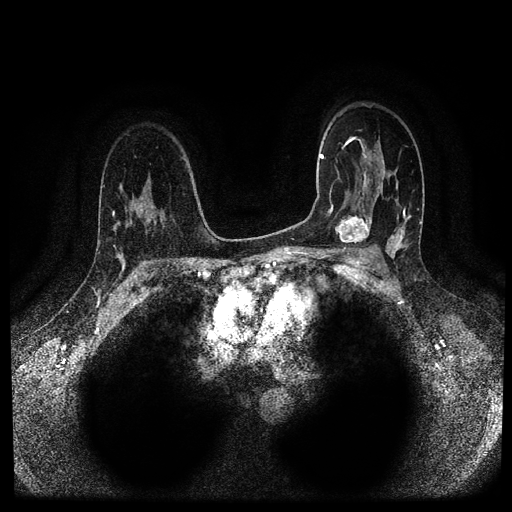
Breast MRI (dynamic contrast-enhanced, multi-phase), one axial slice; slice 69 of 116 in the series (ordered by position); dynamic contrast-enhanced series, time point 2 of 5 at this slice position (early post-contrast); 1.5 T; TE 2.6 ms, TR 5.3 ms; 512 × 512 image matrix. Patient: female, 44 years.
Structures marked on this image (semi-automatic segmentation, software-assisted and operator-edited):
- breast lesion (labelled 'tumour' in the annotation; benign lesions carry a separate 'benign' label): bounding box [x1, y1, x2, y2] px = [334, 211, 374, 248]